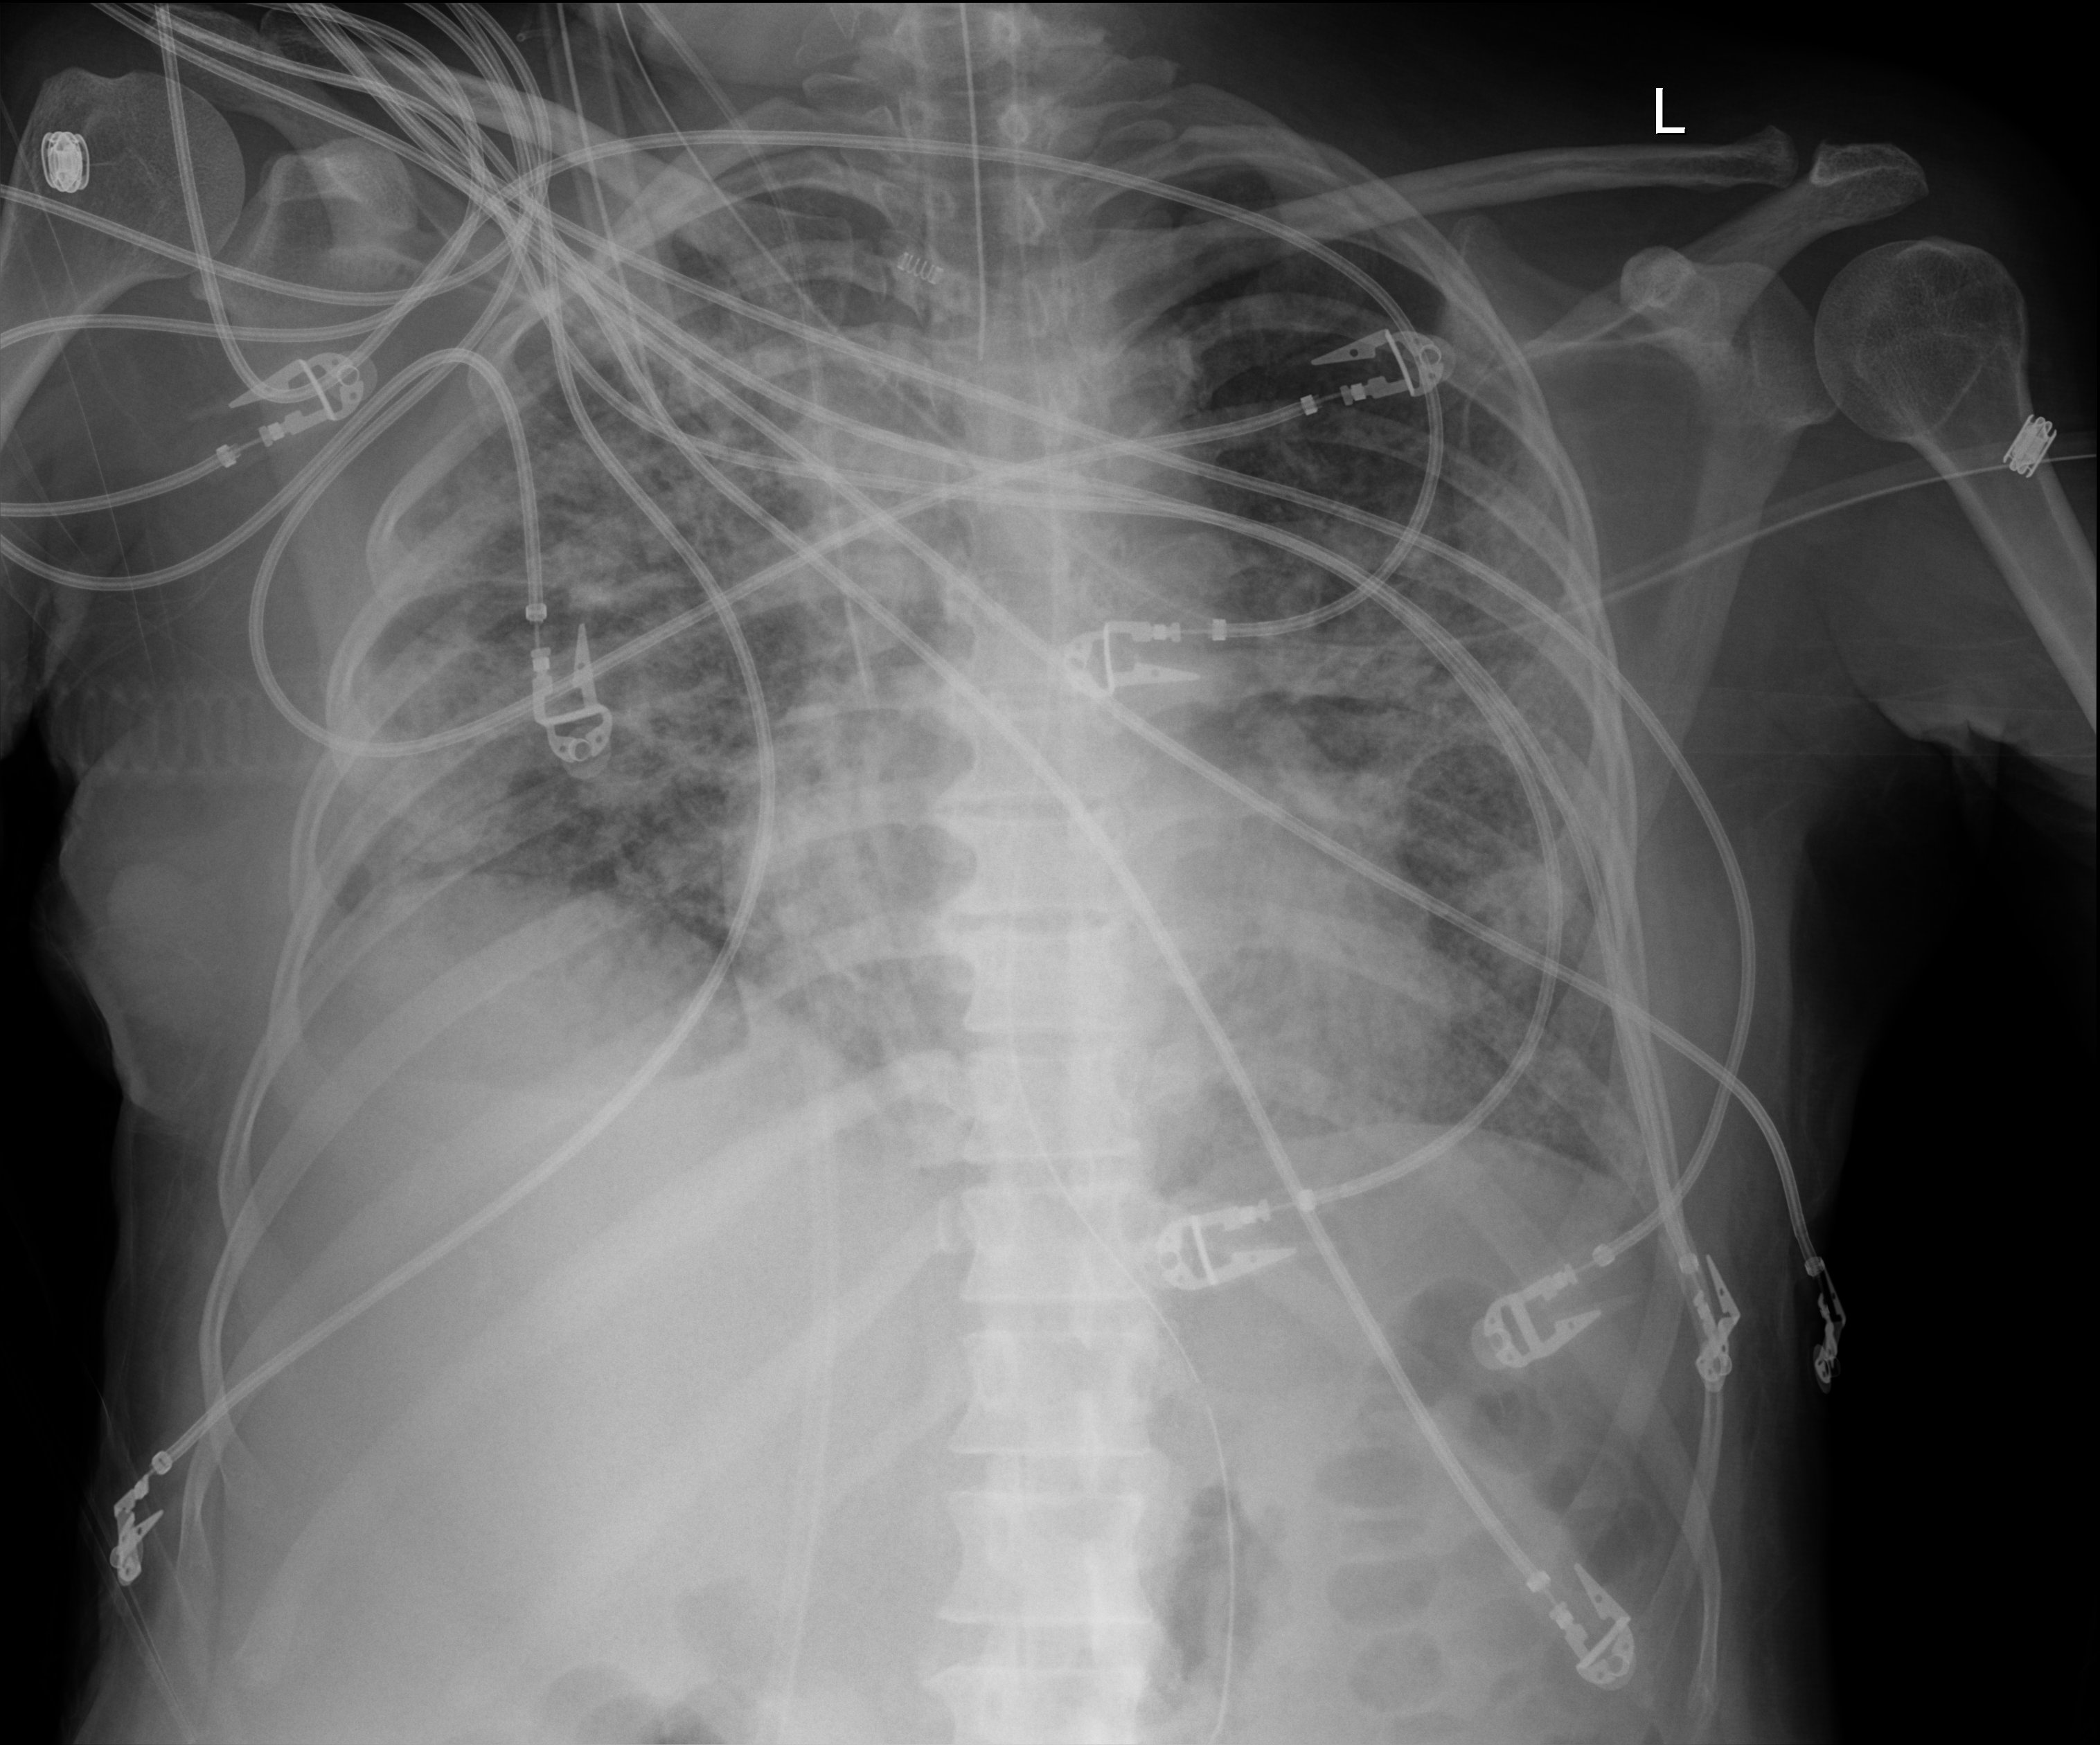
Portable chest radiograph, anteroposterior (AP) projection. Female patient hospitalised with COVID-19, age 18–59 years.
Hospital-stay facts (about this admission, not read from this image; timing relative to this image not recorded):
- chronic kidney disease (admission record): no
- length of hospital stay: 71 days
- COPD (admission record): no